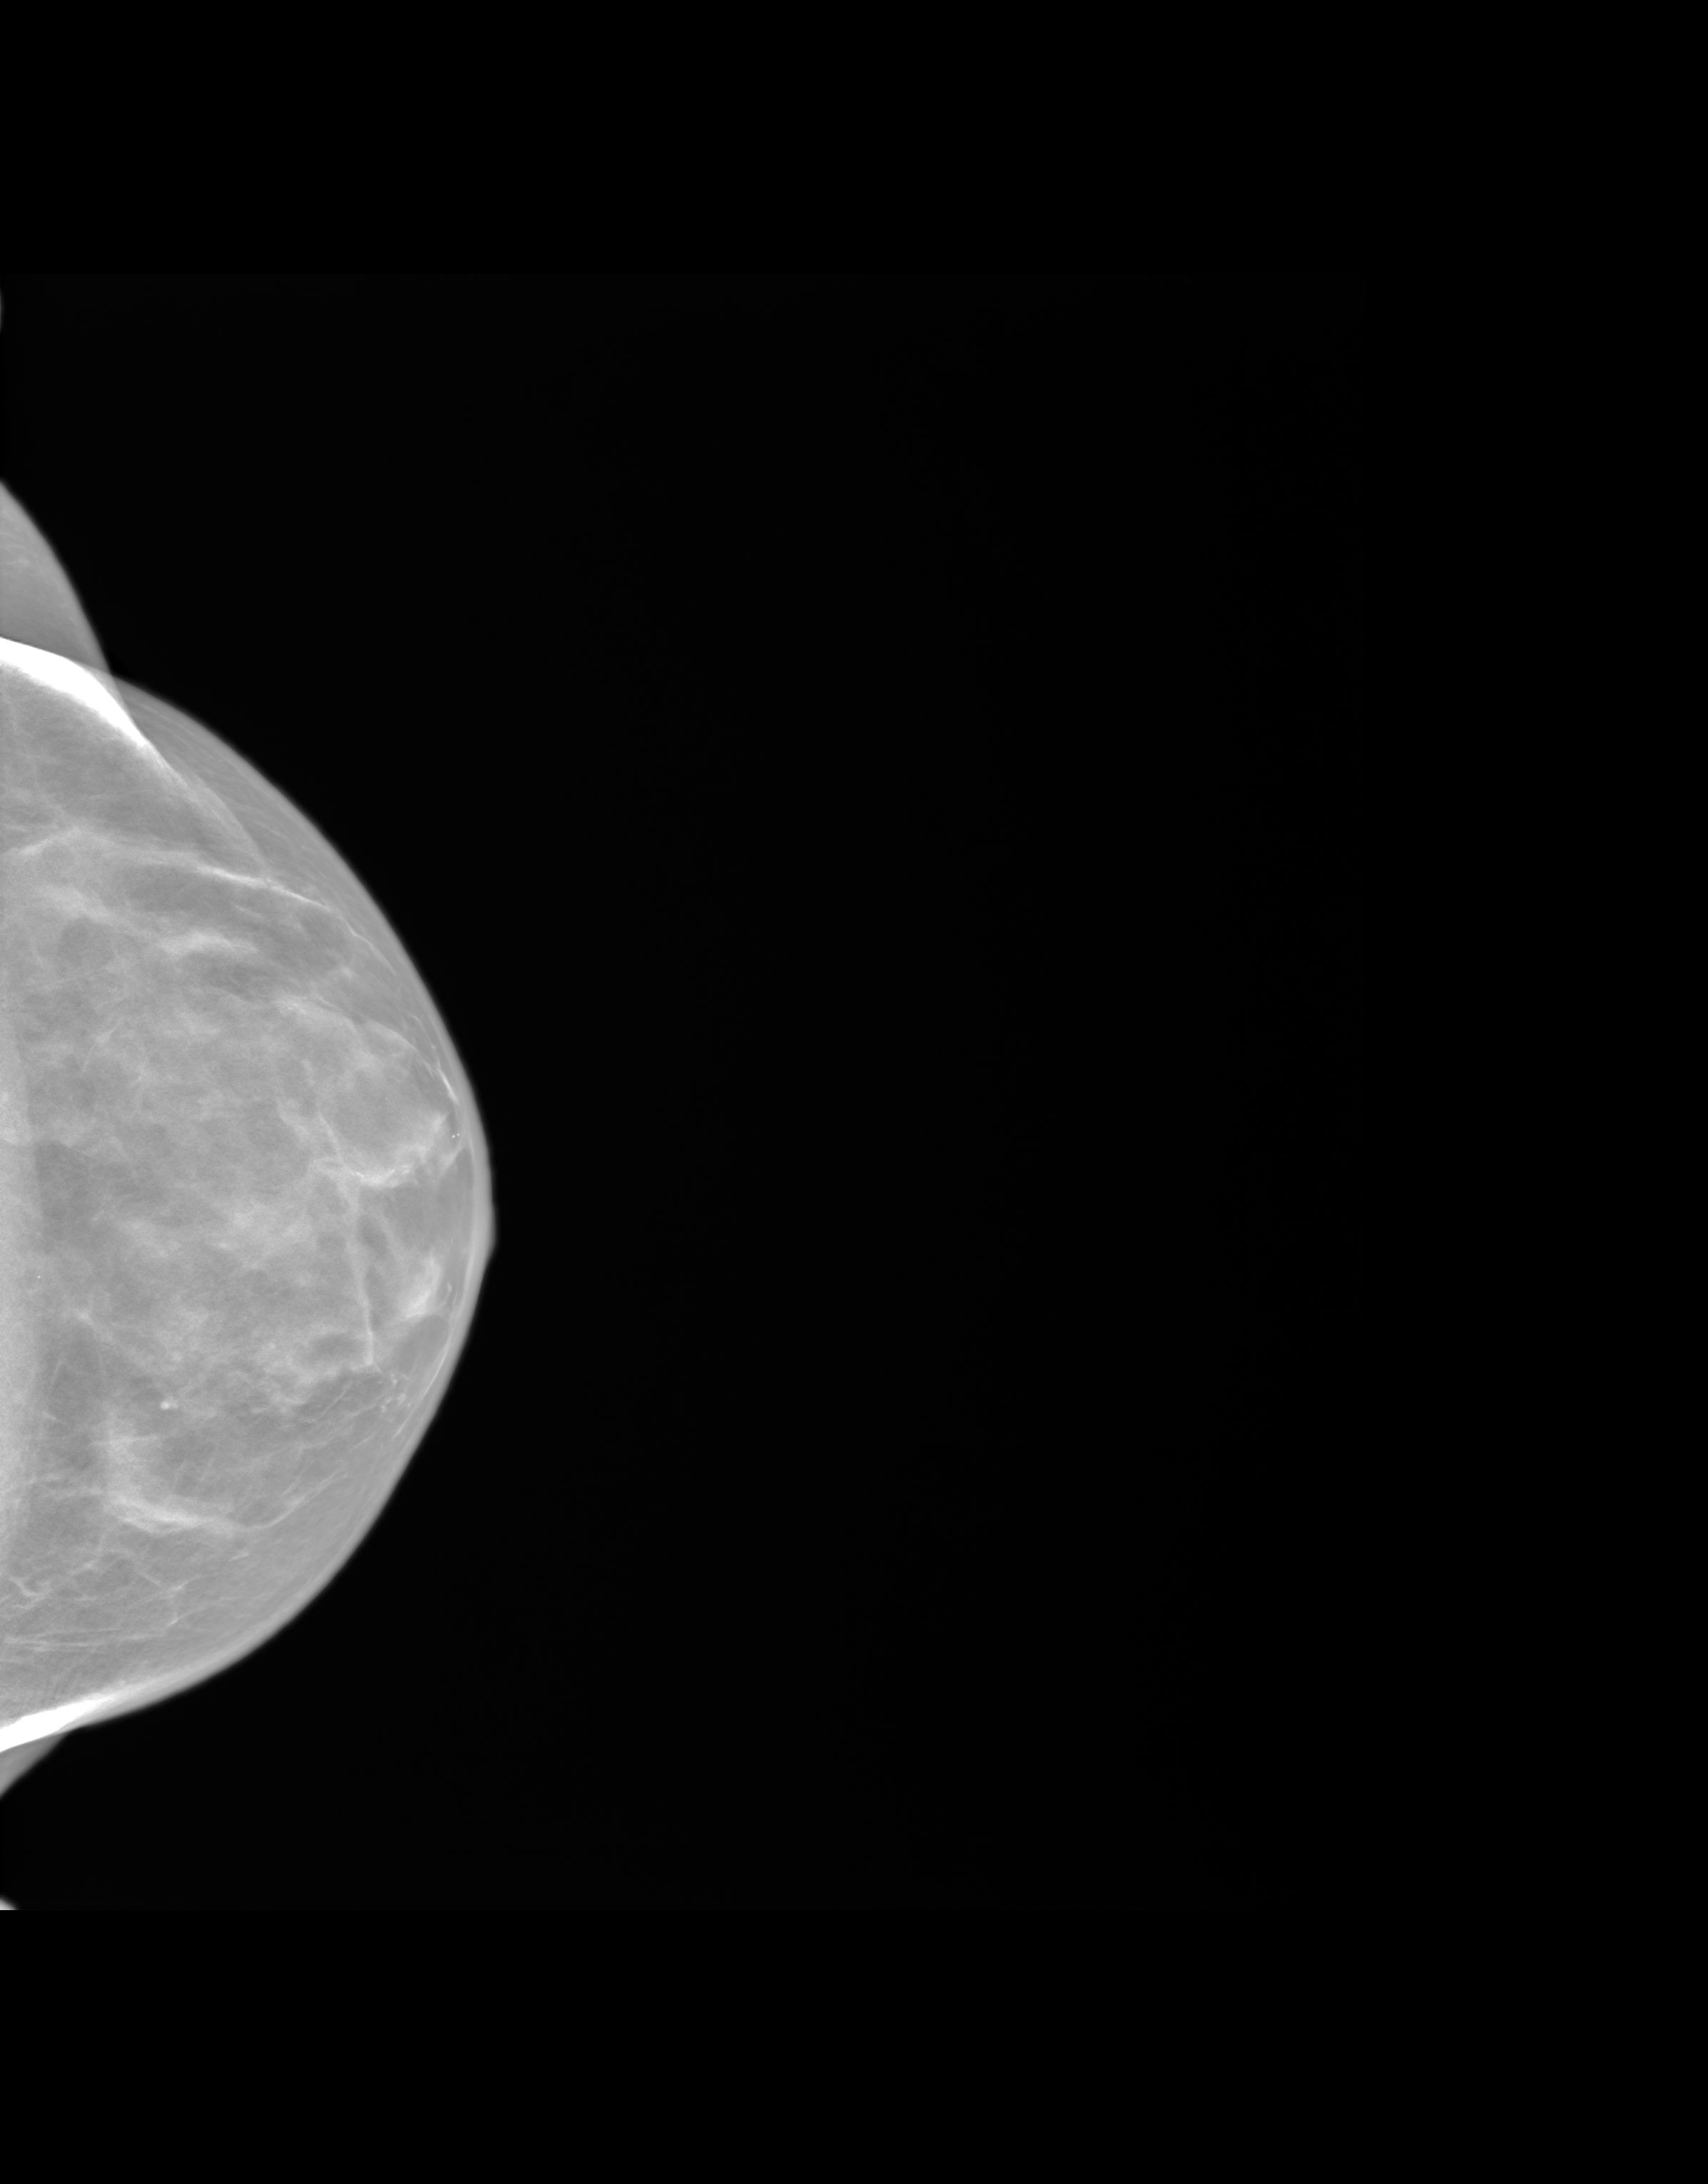
Screening examination. Patient: female, 67 years.
Image type: synthesized 2-D view from tomosynthesis. Breast: left. Projection: CC view.